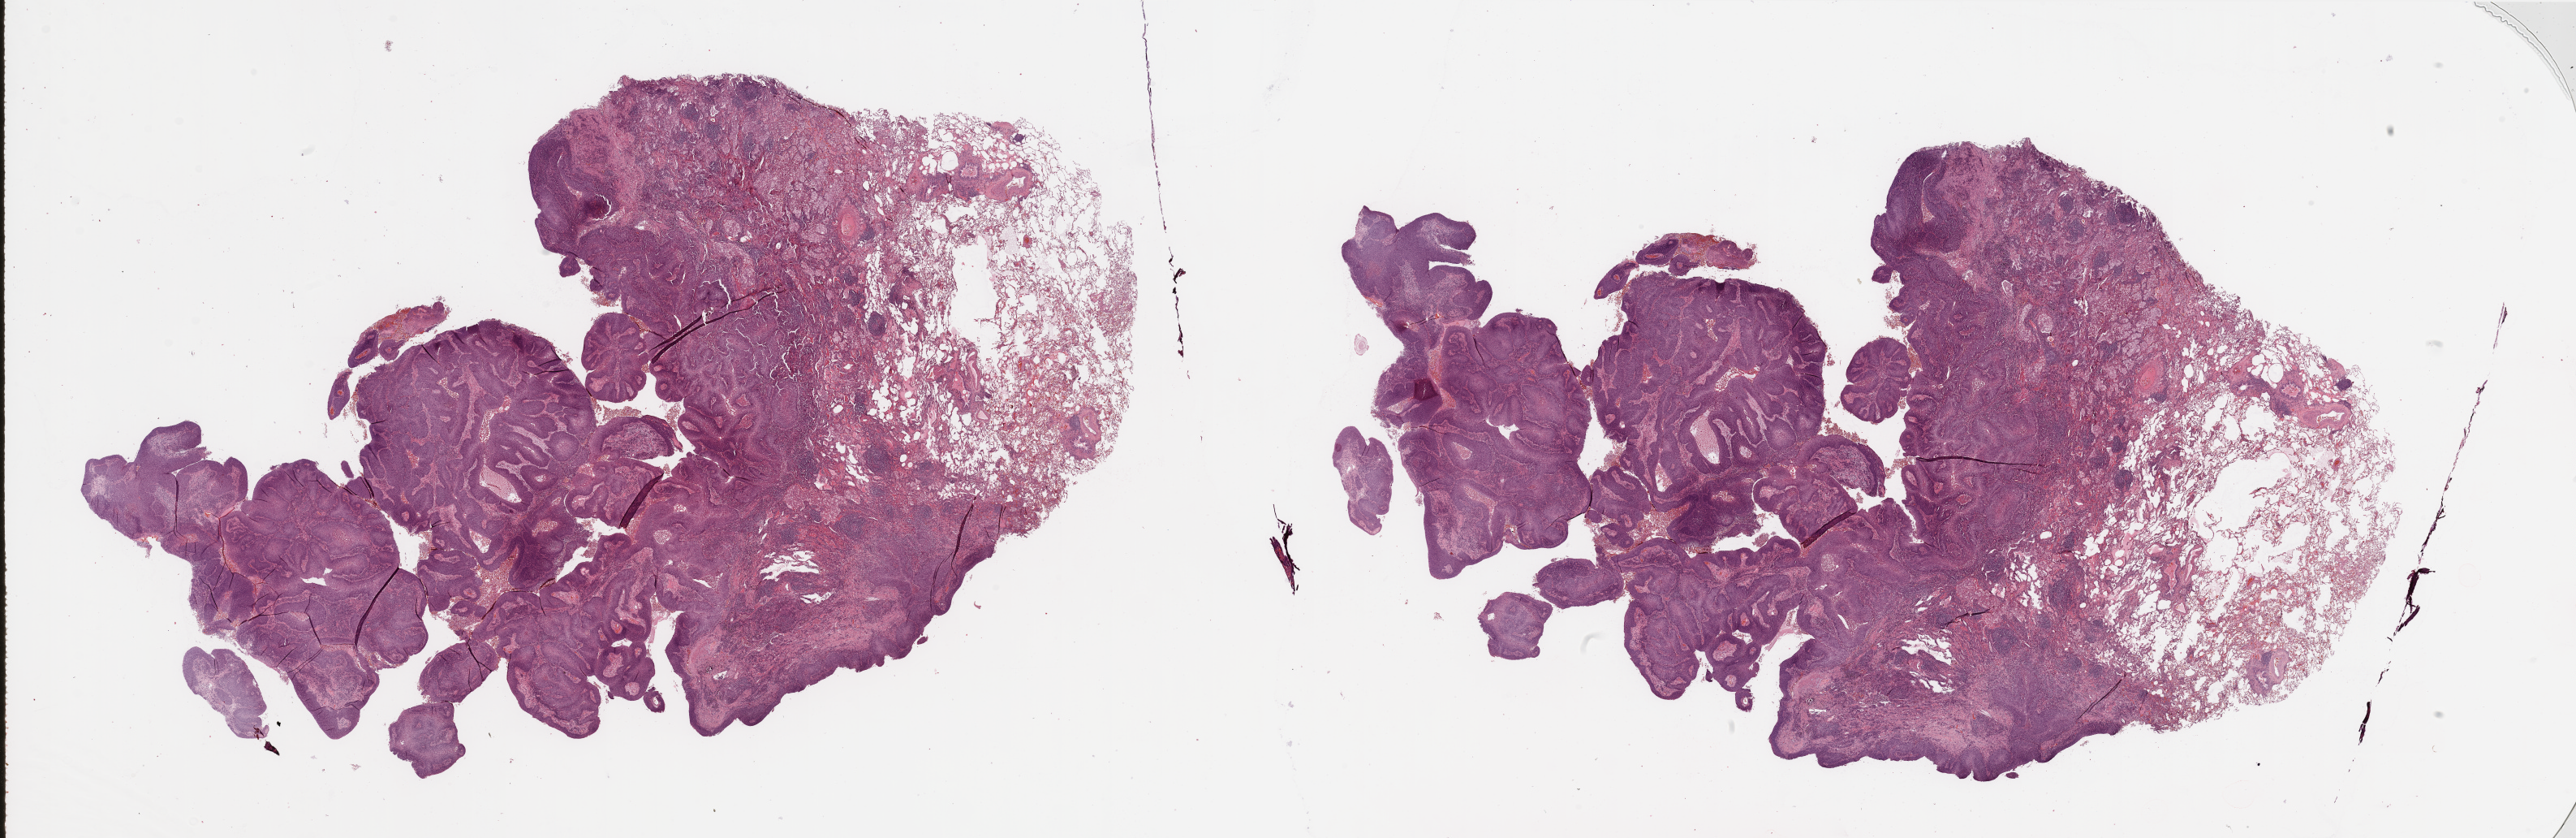
Digitized Hematoxylin and eosin (H&E) stained tissue section (whole slide) — shown as a low-resolution overview of the whole scanned area (about 50.2 x 16.3 mm, acquisition: 20x scan); lung, tumour tissue. Male, 68 y/o.
Patient diagnosis (cohort enrolment): squamous cell carcinoma (lung).